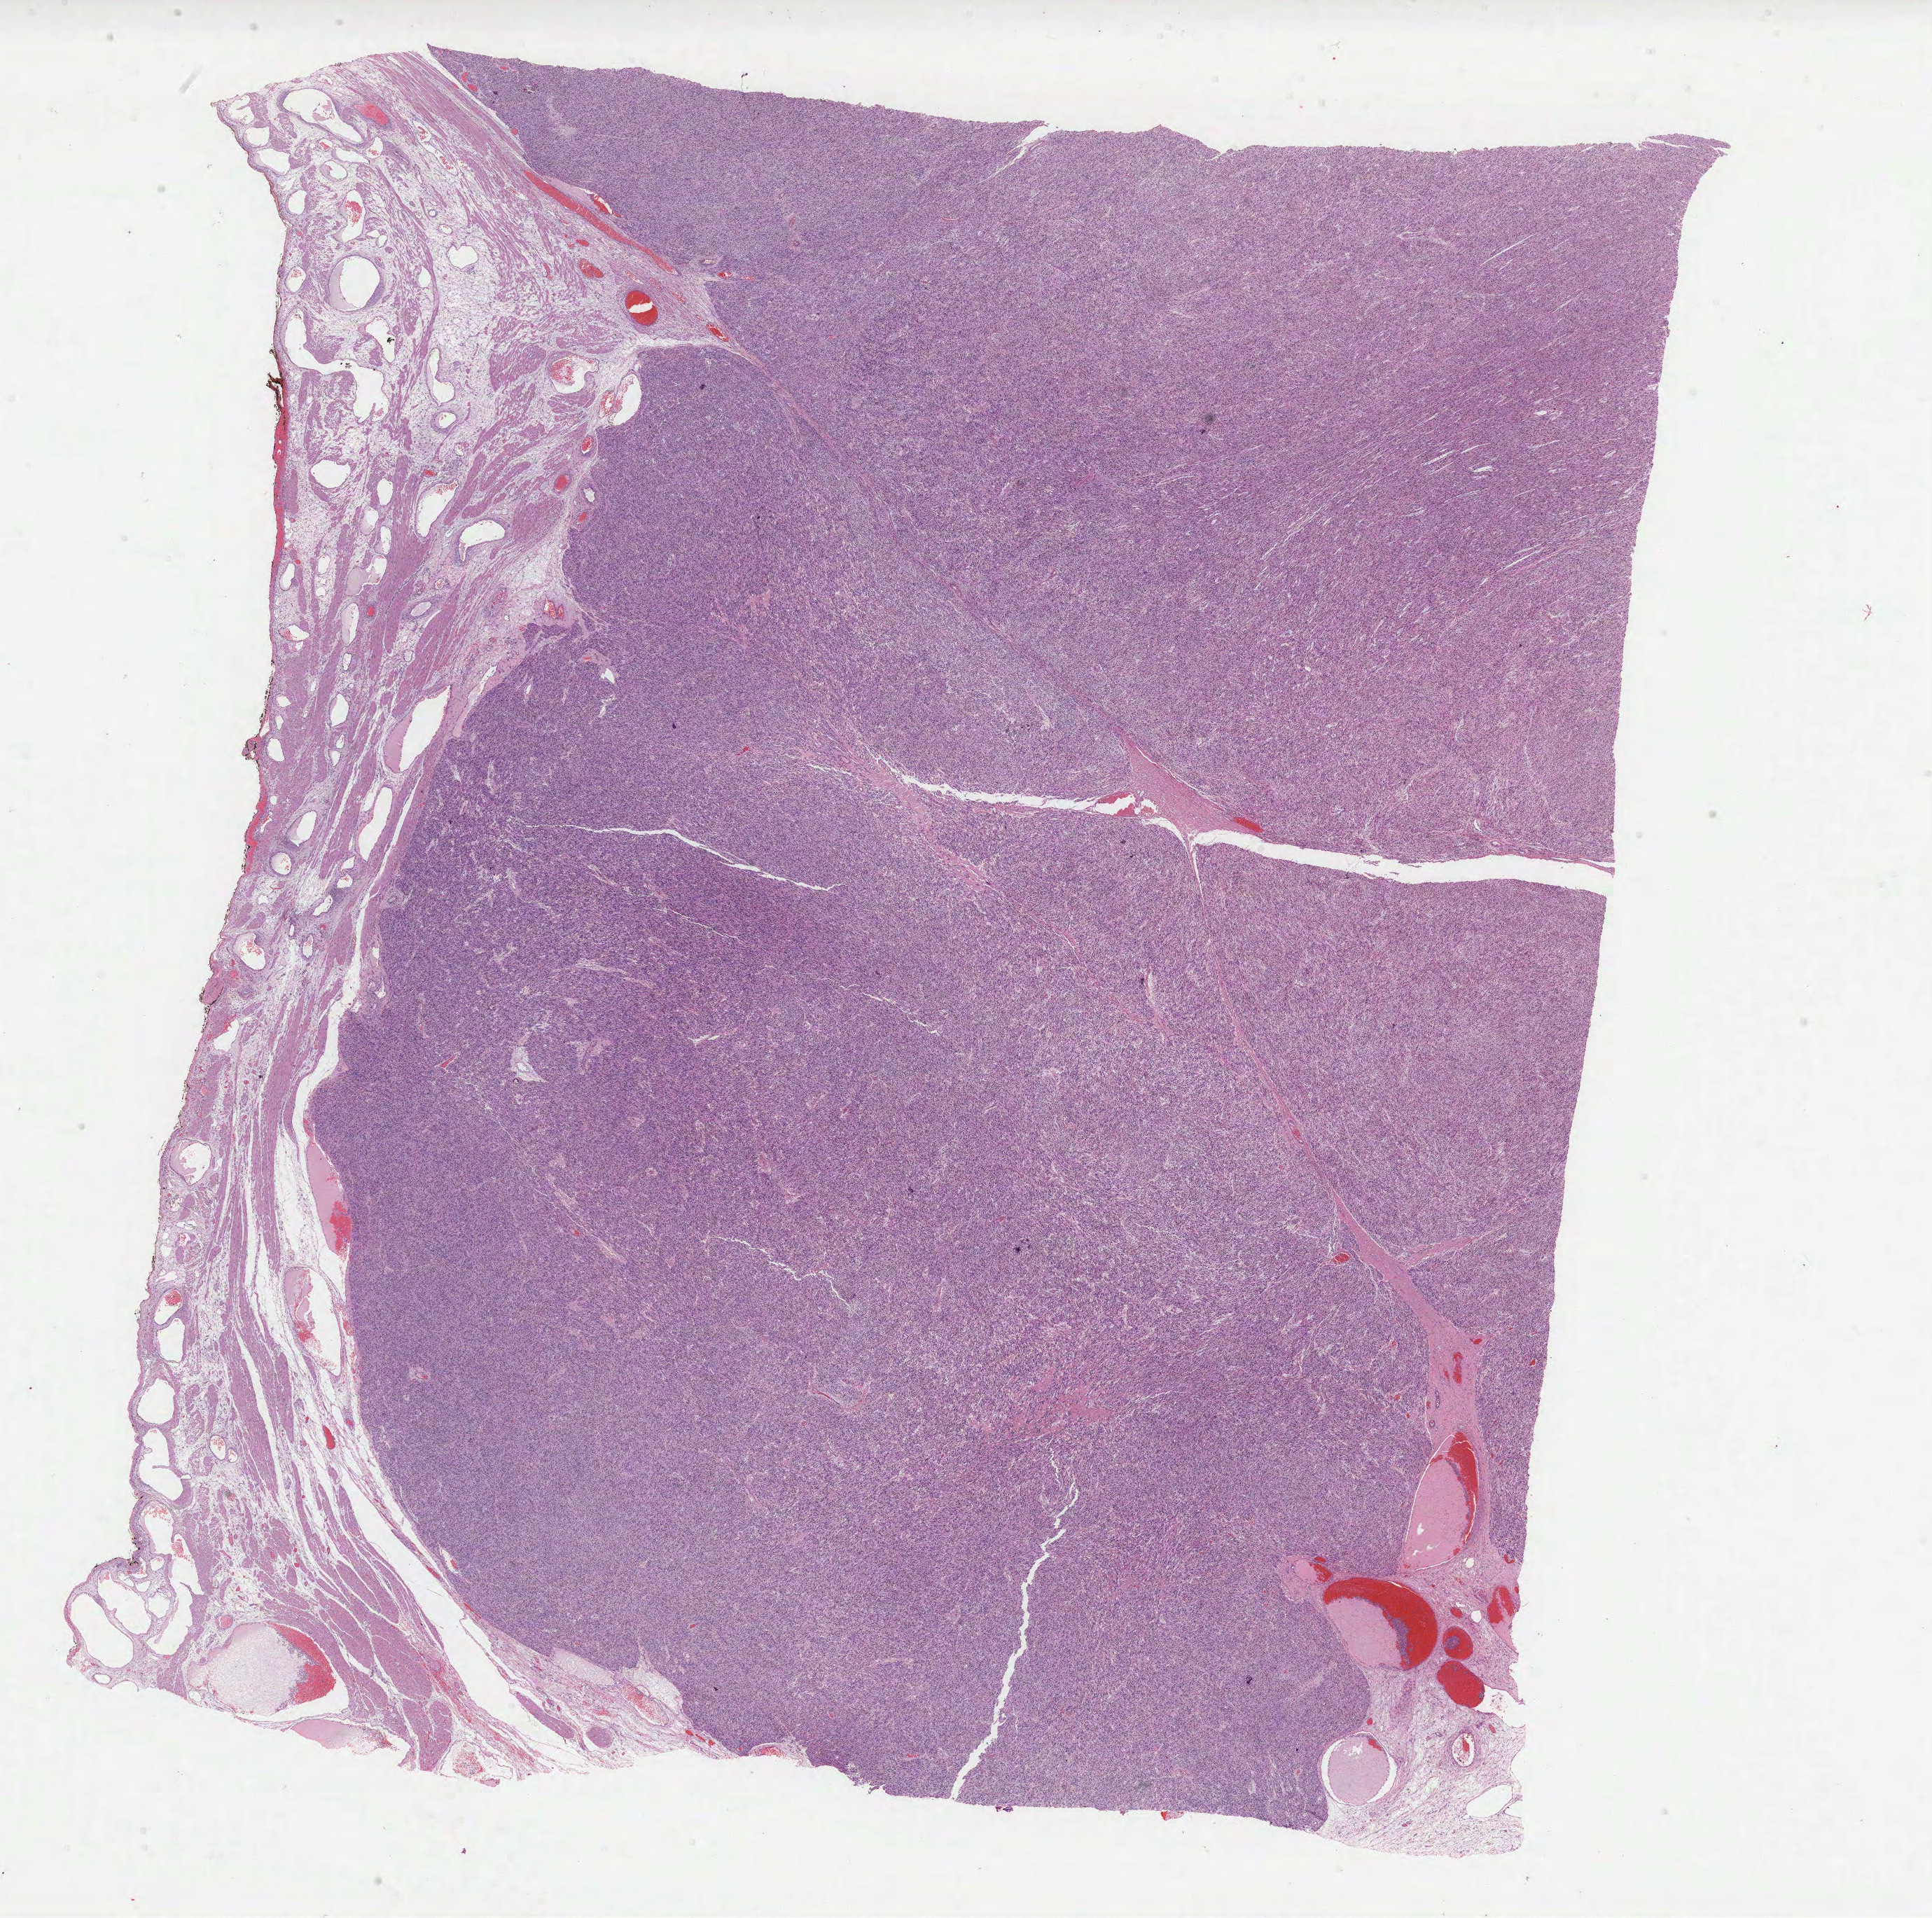
H&E whole-slide image — low-resolution overview of the scanned area, about 22.3 x 22.1 mm, formalin-fixed paraffin-embedded (FFPE) diagnostic section, retroperitoneum and peritoneum, primary tumour sample. Patient: male, age at initial diagnosis 62 years.
Diagnosis: Leiomyosarcoma, NOS (retroperitoneum).